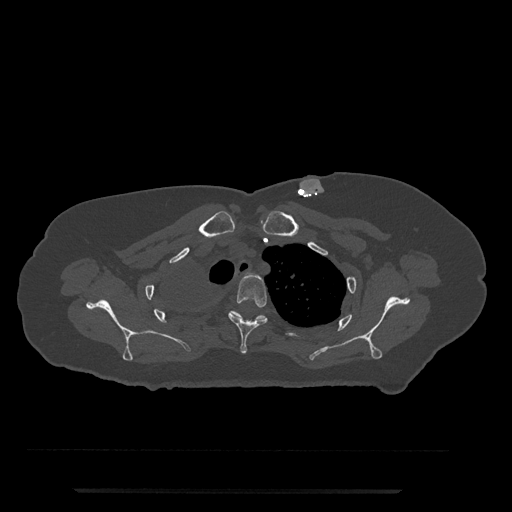
CT including the spine, one axial slice. Slice 625 of 797 in the series (ordered by position). 120 kVp. Bone window (W 1800 / L 400 HU). 0.5 mm slice thickness. 512 × 512 image matrix, field of view 440 × 440 mm. Patient: female, 51 years. From the clinical record (not read from this slice): primary cancer: neuro.
Annotated regions visible in this slice (semi-automatically segmented with operator editing):
- T3 vertebra: bounding box <228,273,268,354> (left, top, right, bottom; pixels)
- T4 vertebra: <229,311,266,319>